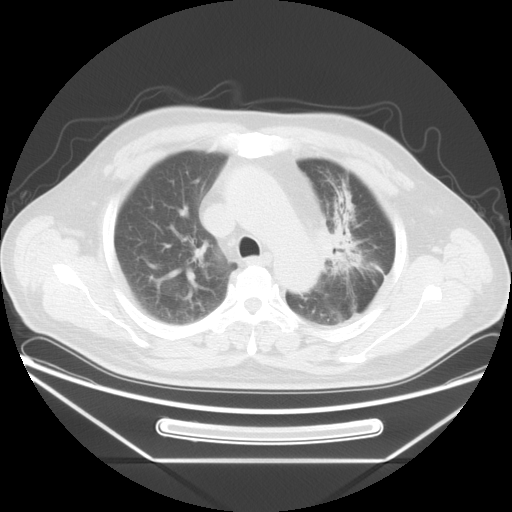
Chest CT, one axial slice; slice 28 of 38 in the series (ordered by position); reconstruction kernel STANDARD; 120 kVp; lung window (W 1500 / L -600 HU); 5 mm slice thickness; 512 × 512 image matrix. Patient: male, 61 years. Case-level facts recorded for this patient, not image findings: clinical TNM (as recorded): T2a N0 M0.
Structures marked on this image (rectangle marked by the reading radiologist):
- lung tumour (recorded histology: small cell carcinoma): box from (x=326, y=190) to (x=367, y=276) px